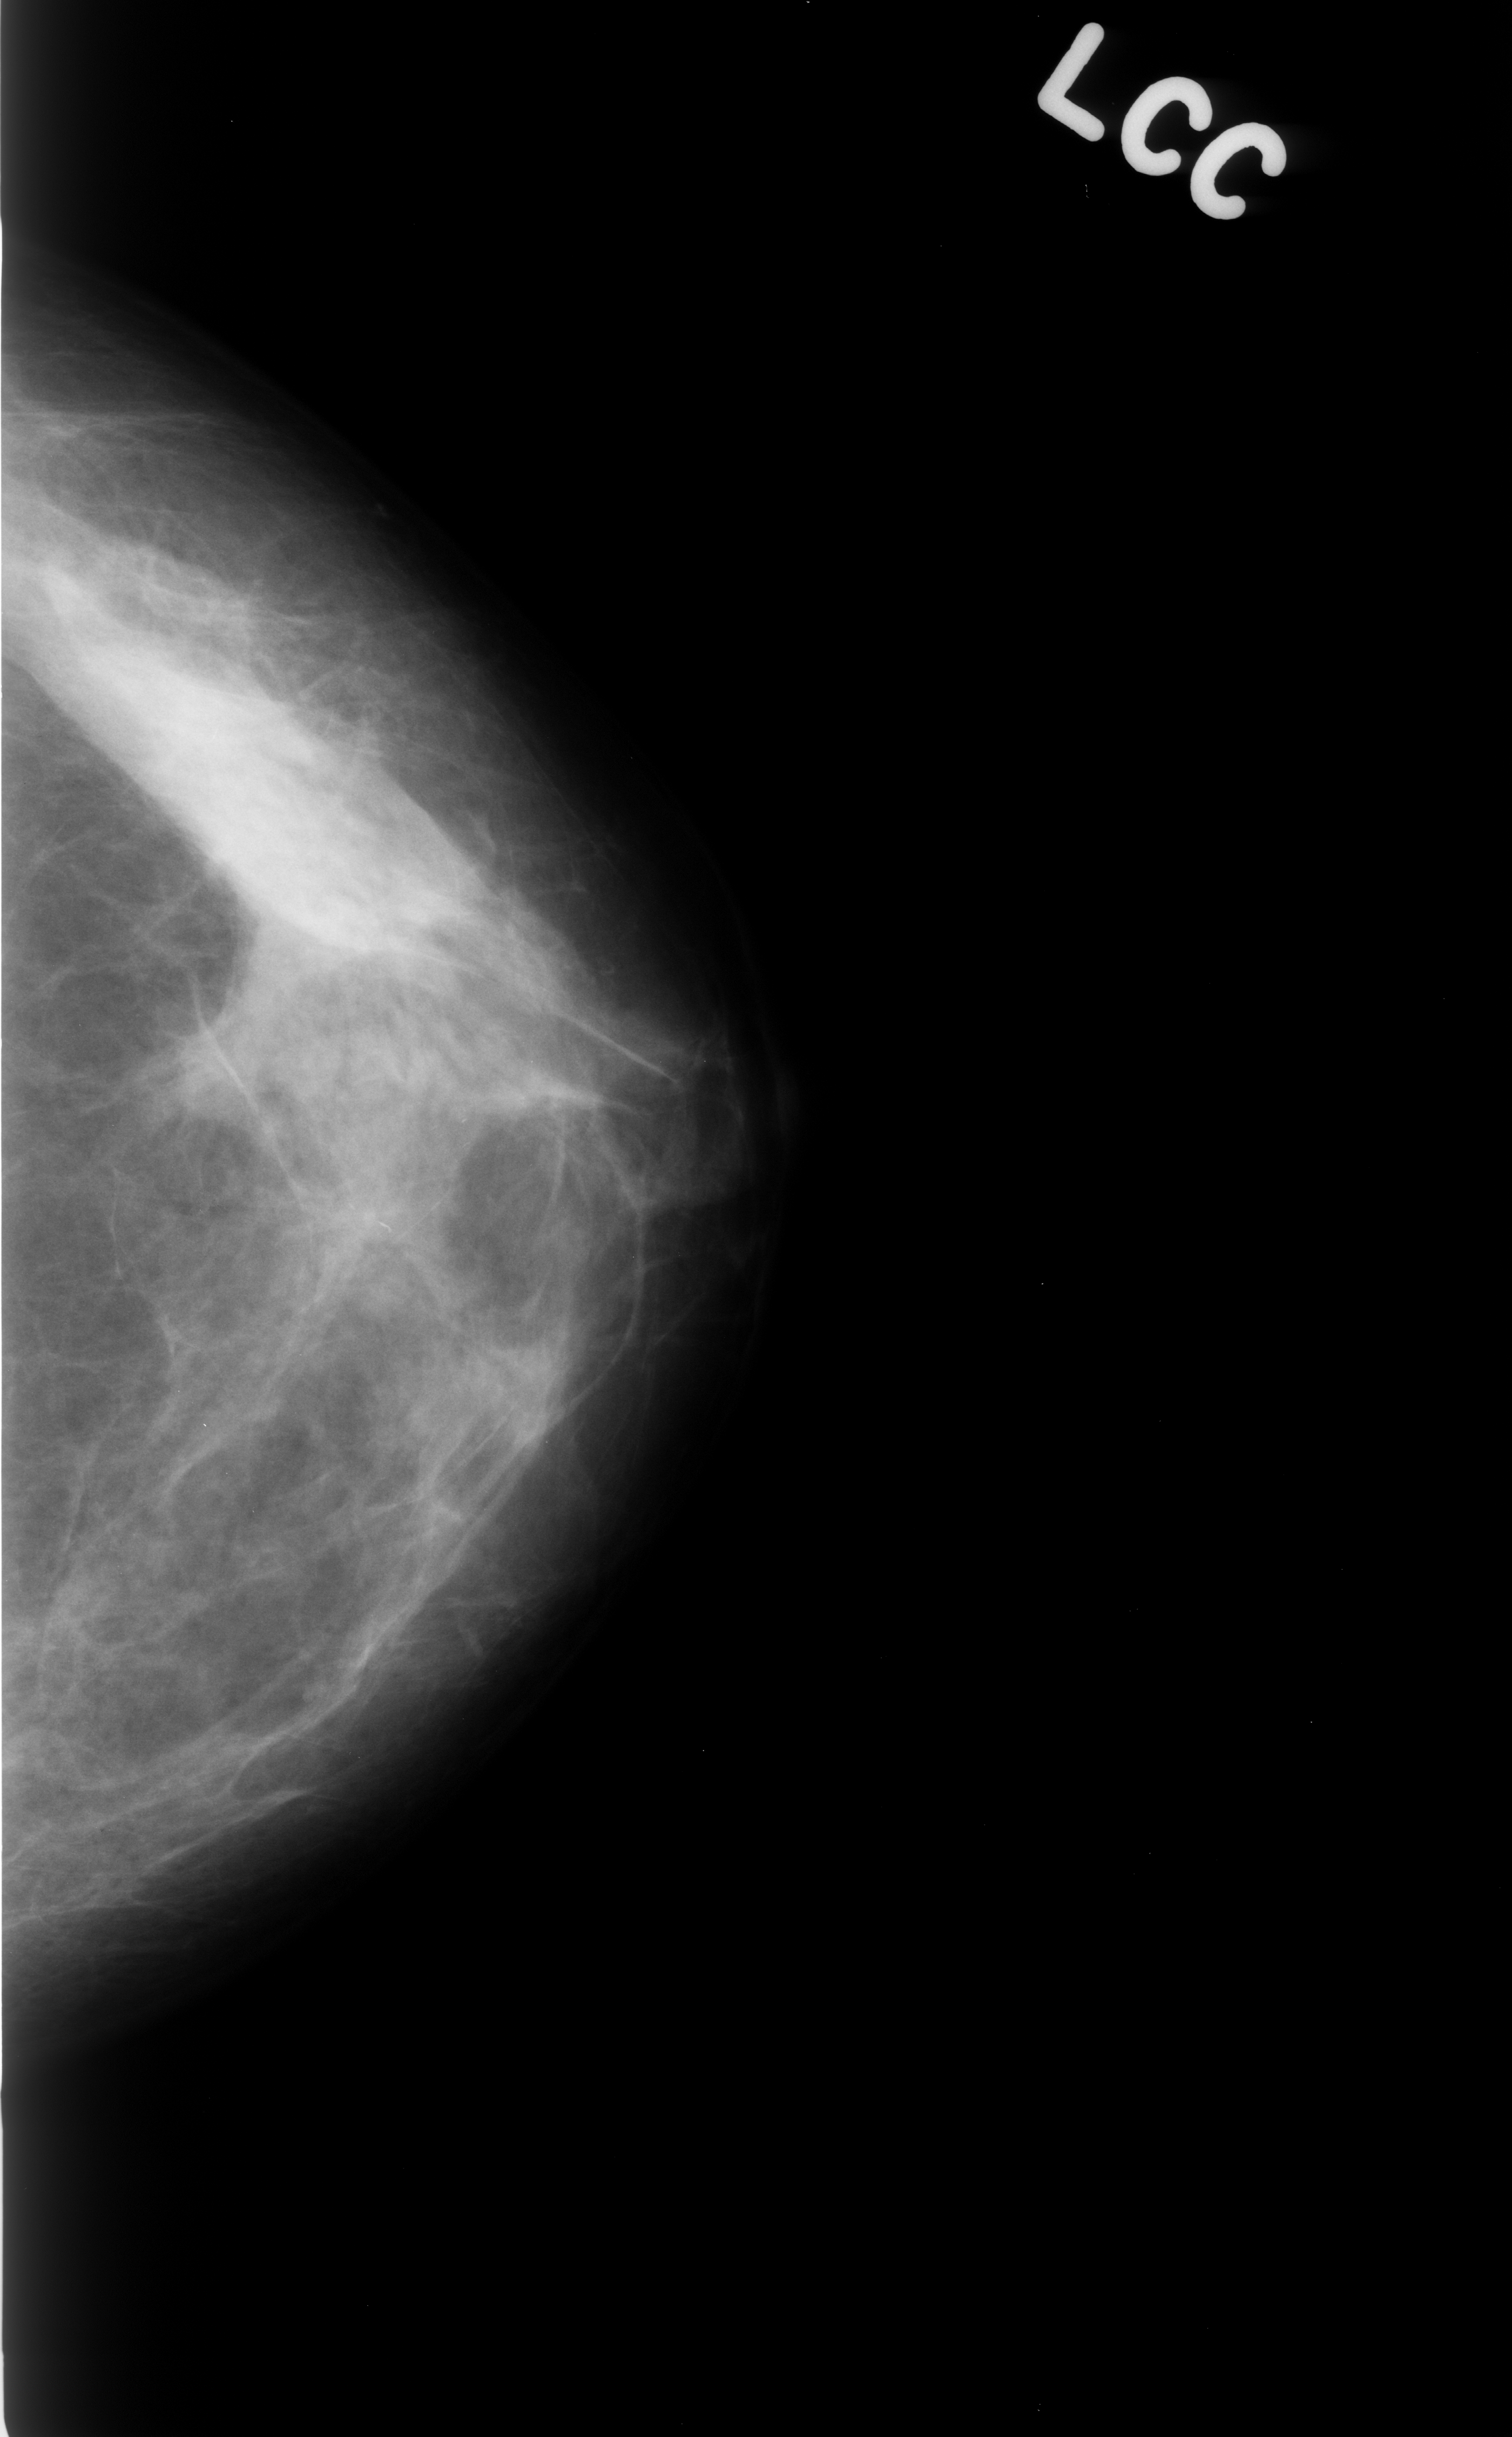
Digitized screen-film mammogram; left breast; CC view; breast composition: scattered fibroglandular densities (BI-RADS density category 2 of 4); 1512 × 2437 image matrix.
Expert-marked regions of interest on this film, with their recorded descriptors:
- Finding 1 of 2: calcifications, morphology fine linear branching, distribution linear; BI-RADS assessment category 4; subtlety rating 4 on a 1 (subtle) to 5 (obvious) scale; pathology result (as recorded, not read from the image): benign: bounding box [x1, y1, x2, y2] px = [99, 600, 329, 887]
- Finding 2 of 2: calcifications, morphology fine linear branching, distribution linear; BI-RADS assessment category 4; subtlety rating 4 on a 1 (subtle) to 5 (obvious) scale; pathology (as recorded): benign: [237, 1027, 563, 1332]